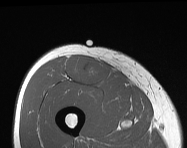
MRI of an extremity soft-tissue mass, one axial slice. Position 60 of 114 along the scan axis. MR volume resampled by the dataset authors to the PET/CT grid (not the native acquisition matrix). 3.27 mm slice thickness. 187 × 148 image matrix. Male patient. From the clinical record (not read from this slice): histological type: pleiomorphic leiomyosarcoma; grade: intermediate; site of the primary tumour: right thigh.
Annotated regions visible in this slice (expert contour drawn on MRI and transferred to this co-registered scan by the dataset authors):
- gross tumour volume including surrounding oedema: box from (x=66, y=56) to (x=112, y=85) px